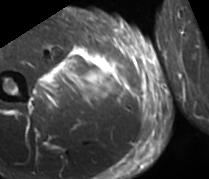
MRI of an extremity soft-tissue mass, one axial slice; position 28 of 89 along the scan axis; STIR; MR volume resampled by the dataset authors to the PET/CT grid (not the native acquisition matrix); 3.27 mm slice thickness; 209 × 179 image matrix. Male patient. Case-level facts recorded for this patient, not image findings: histological type: undifferentiated - pleiomorphic; grade: high; site of the primary tumour: right thigh.
Structures marked on this image (expert contour drawn on MRI and transferred to this co-registered scan by the dataset authors):
- gross tumour volume including surrounding oedema: bounding box (x1, y1, x2, y2) in pixels: (32, 46, 113, 104)
- gross tumour volume (mass): (85, 71, 109, 88)